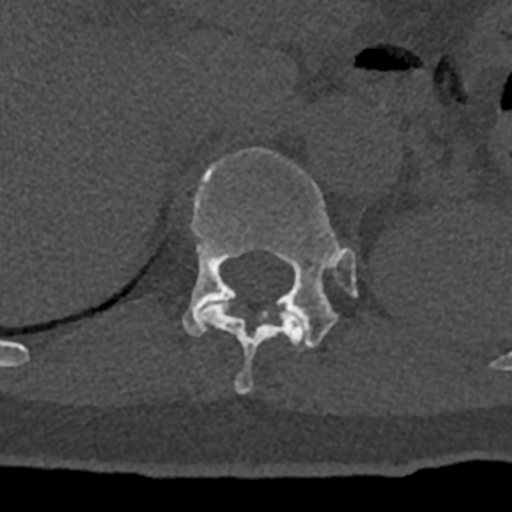
CT including the spine, one axial slice. Slice 514 of 797 in the series (ordered by position). Reconstruction kernel Br40s/3. Bone window (W 1800 / L 400 HU). 0.5 mm slice thickness. 512 × 512 image matrix, field of view 160 × 160 mm. Male patient, age 74 years. Case-level facts recorded for this patient, not image findings: primary cancer: renal; vertebrae with lytic lesions (as recorded): T10, L1, L2, L3, L4, L5.
Structures marked on this image (semi-automatic segmentation, software-assisted and operator-edited):
- T11 vertebra: box from (x=199, y=301) to (x=305, y=394) px
- T12 vertebra: (x=182, y=147)–(x=358, y=348)